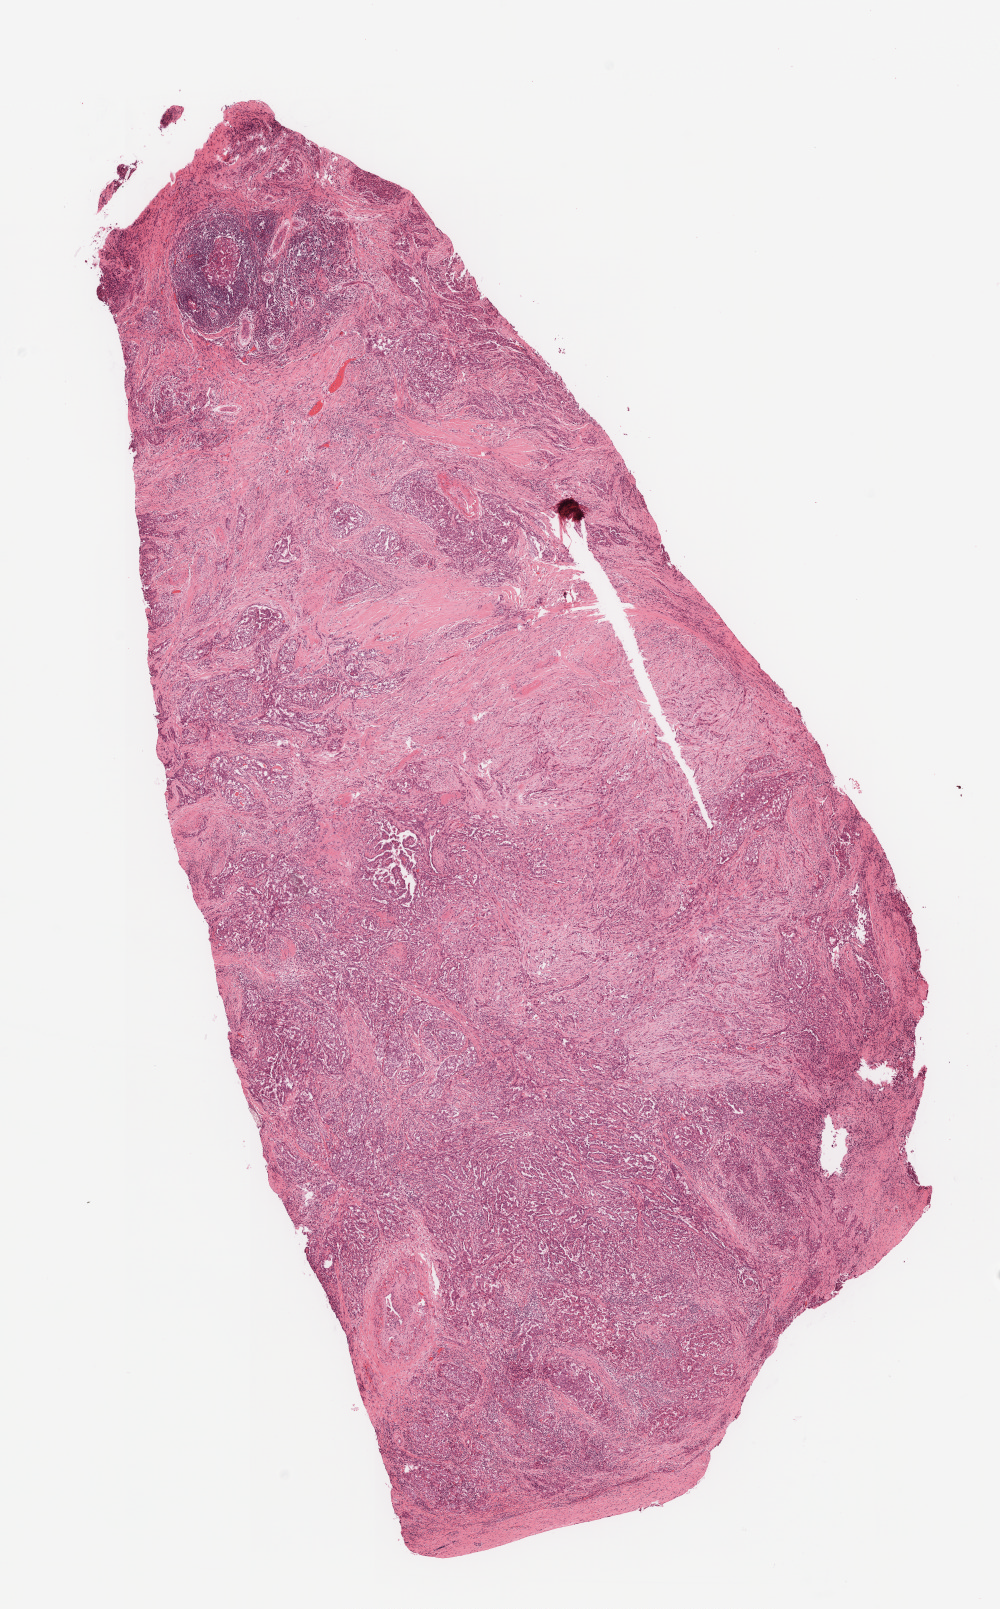
Whole-slide histology image, Hematoxylin and eosin (H&E) stained — whole scanned area (about 8.0 x 12.9 mm) shown as a low-resolution overview, formalin-fixed paraffin-embedded (FFPE) diagnostic section, thyroid, primary tumour sample. Patient: female, age at initial diagnosis 83 years.
Histologic diagnosis: Papillary adenocarcinoma, NOS (thyroid gland). Lymph nodes positive (case pathology): 3 of 16 examined. TNM: T2 N1a MX. AJCC pathologic stage: III (7th edition).